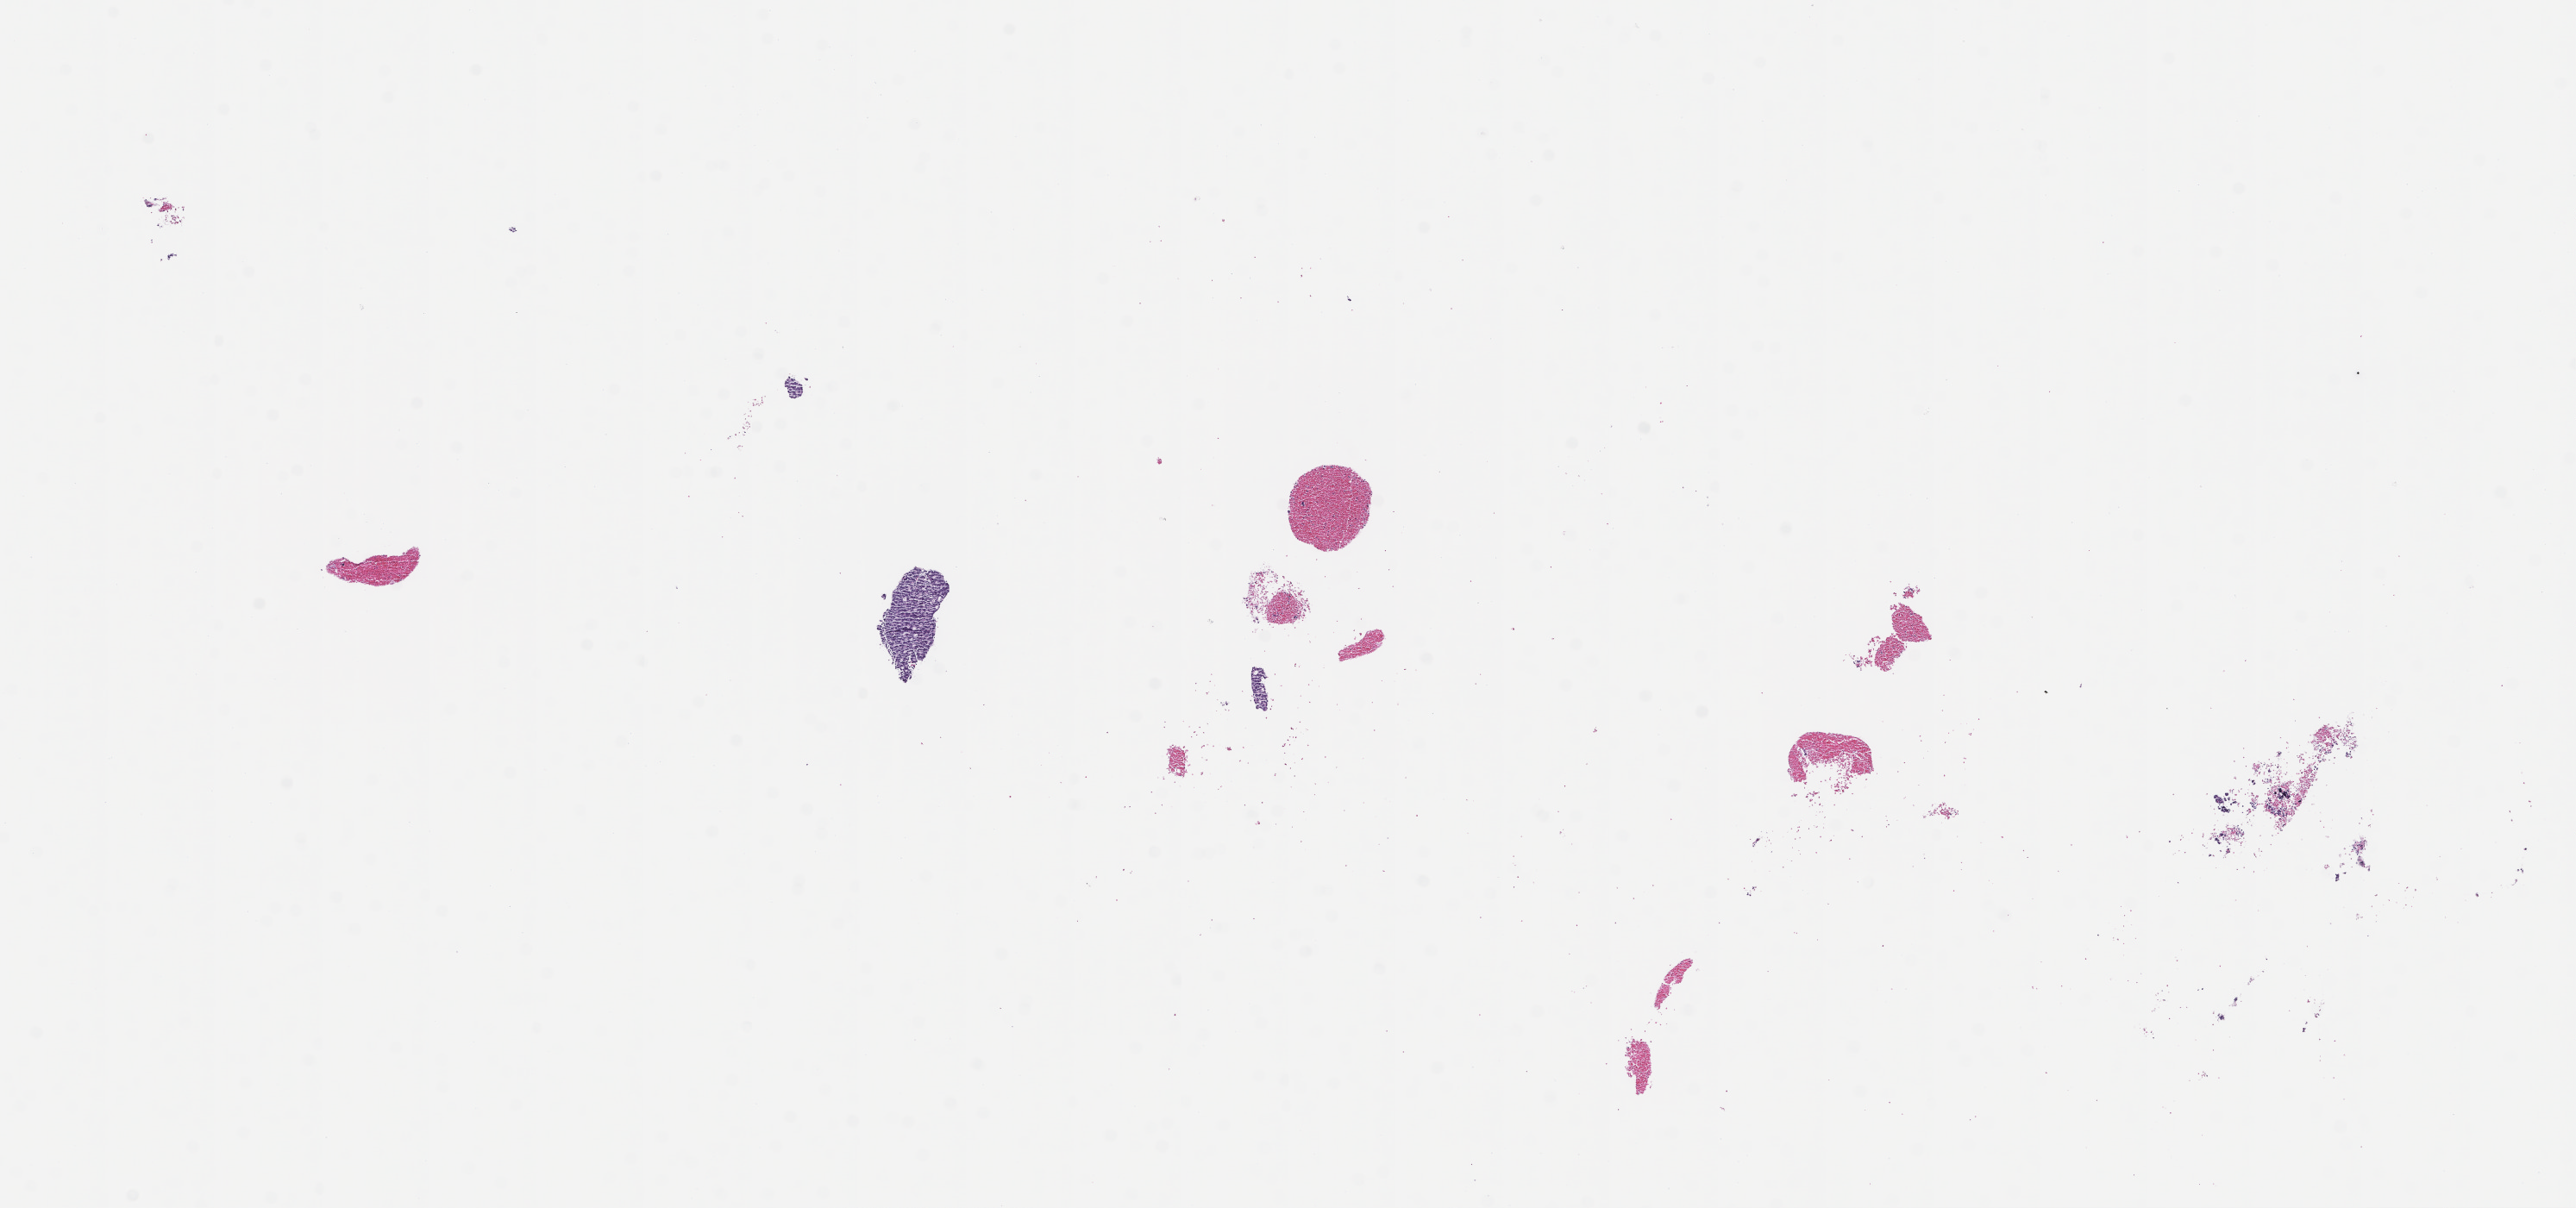
Hematoxylin and eosin (H&E) whole-slide image — a low-resolution overview of the entire scanned area, about 12.1 x 5.7 mm; formalin-fixed, paraffin-embedded (FFPE) tissue; site: prostate; specimen time point: archival tissue. Patient sex: male.
This section: primary tumor. Diagnosis: Prostate Carcinoma.